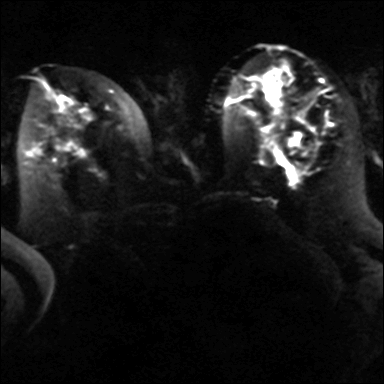
Breast MRI, one axial slice. Position 20 of 40 along the scan axis. Diffusion-weighted series; image 2 of 4 stored at this slice position (different b-values; order by instance number). 3 T. 384 × 384 image matrix, field of view 320 × 320 mm. Female patient.
Outlined on this slice (expert manual segmentation):
- tumour on diffusion-weighted imaging: bounding box [x1, y1, x2, y2] px = [289, 133, 300, 146]